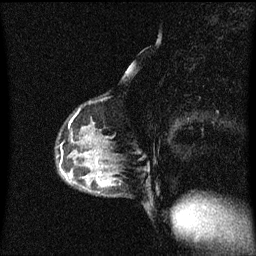
Breast MRI (dynamic contrast-enhanced), one sagittal slice. Dynamic contrast-enhanced series, image 2 of 3 at this slice position (ordered by acquisition). 1.5 T. TE 4.2 ms, TR 8.4 ms. 2 mm slice thickness. 256 × 256 image matrix, field of view 200 × 200 mm. Patient: female, 40 years.
Outlined on this slice (semi-automatically segmented with operator editing):
- analysis volume of interest (the breast-tissue region the enhancement analysis was run in; not a lesion): bounding box (x1, y1, x2, y2) in pixels: (82, 172, 121, 197)
- tumour enhancement mask (voxels above the 70 % enhancement threshold inside the analysis volume of interest): (97, 172, 103, 187)